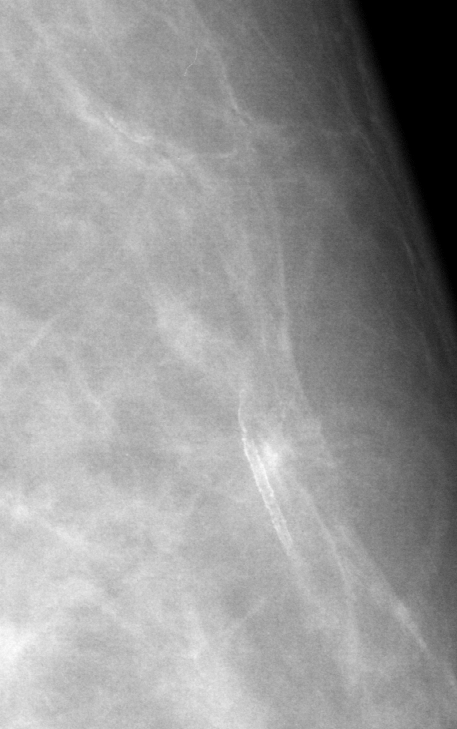
Crop from a digitized film mammogram around one marked abnormality; left breast; MLO view.
Finding: calcifications, morphology vascular; BI-RADS assessment category 2; subtlety rating 5 on a 1 (subtle) to 5 (obvious) scale; benign without callback (not worked up further).